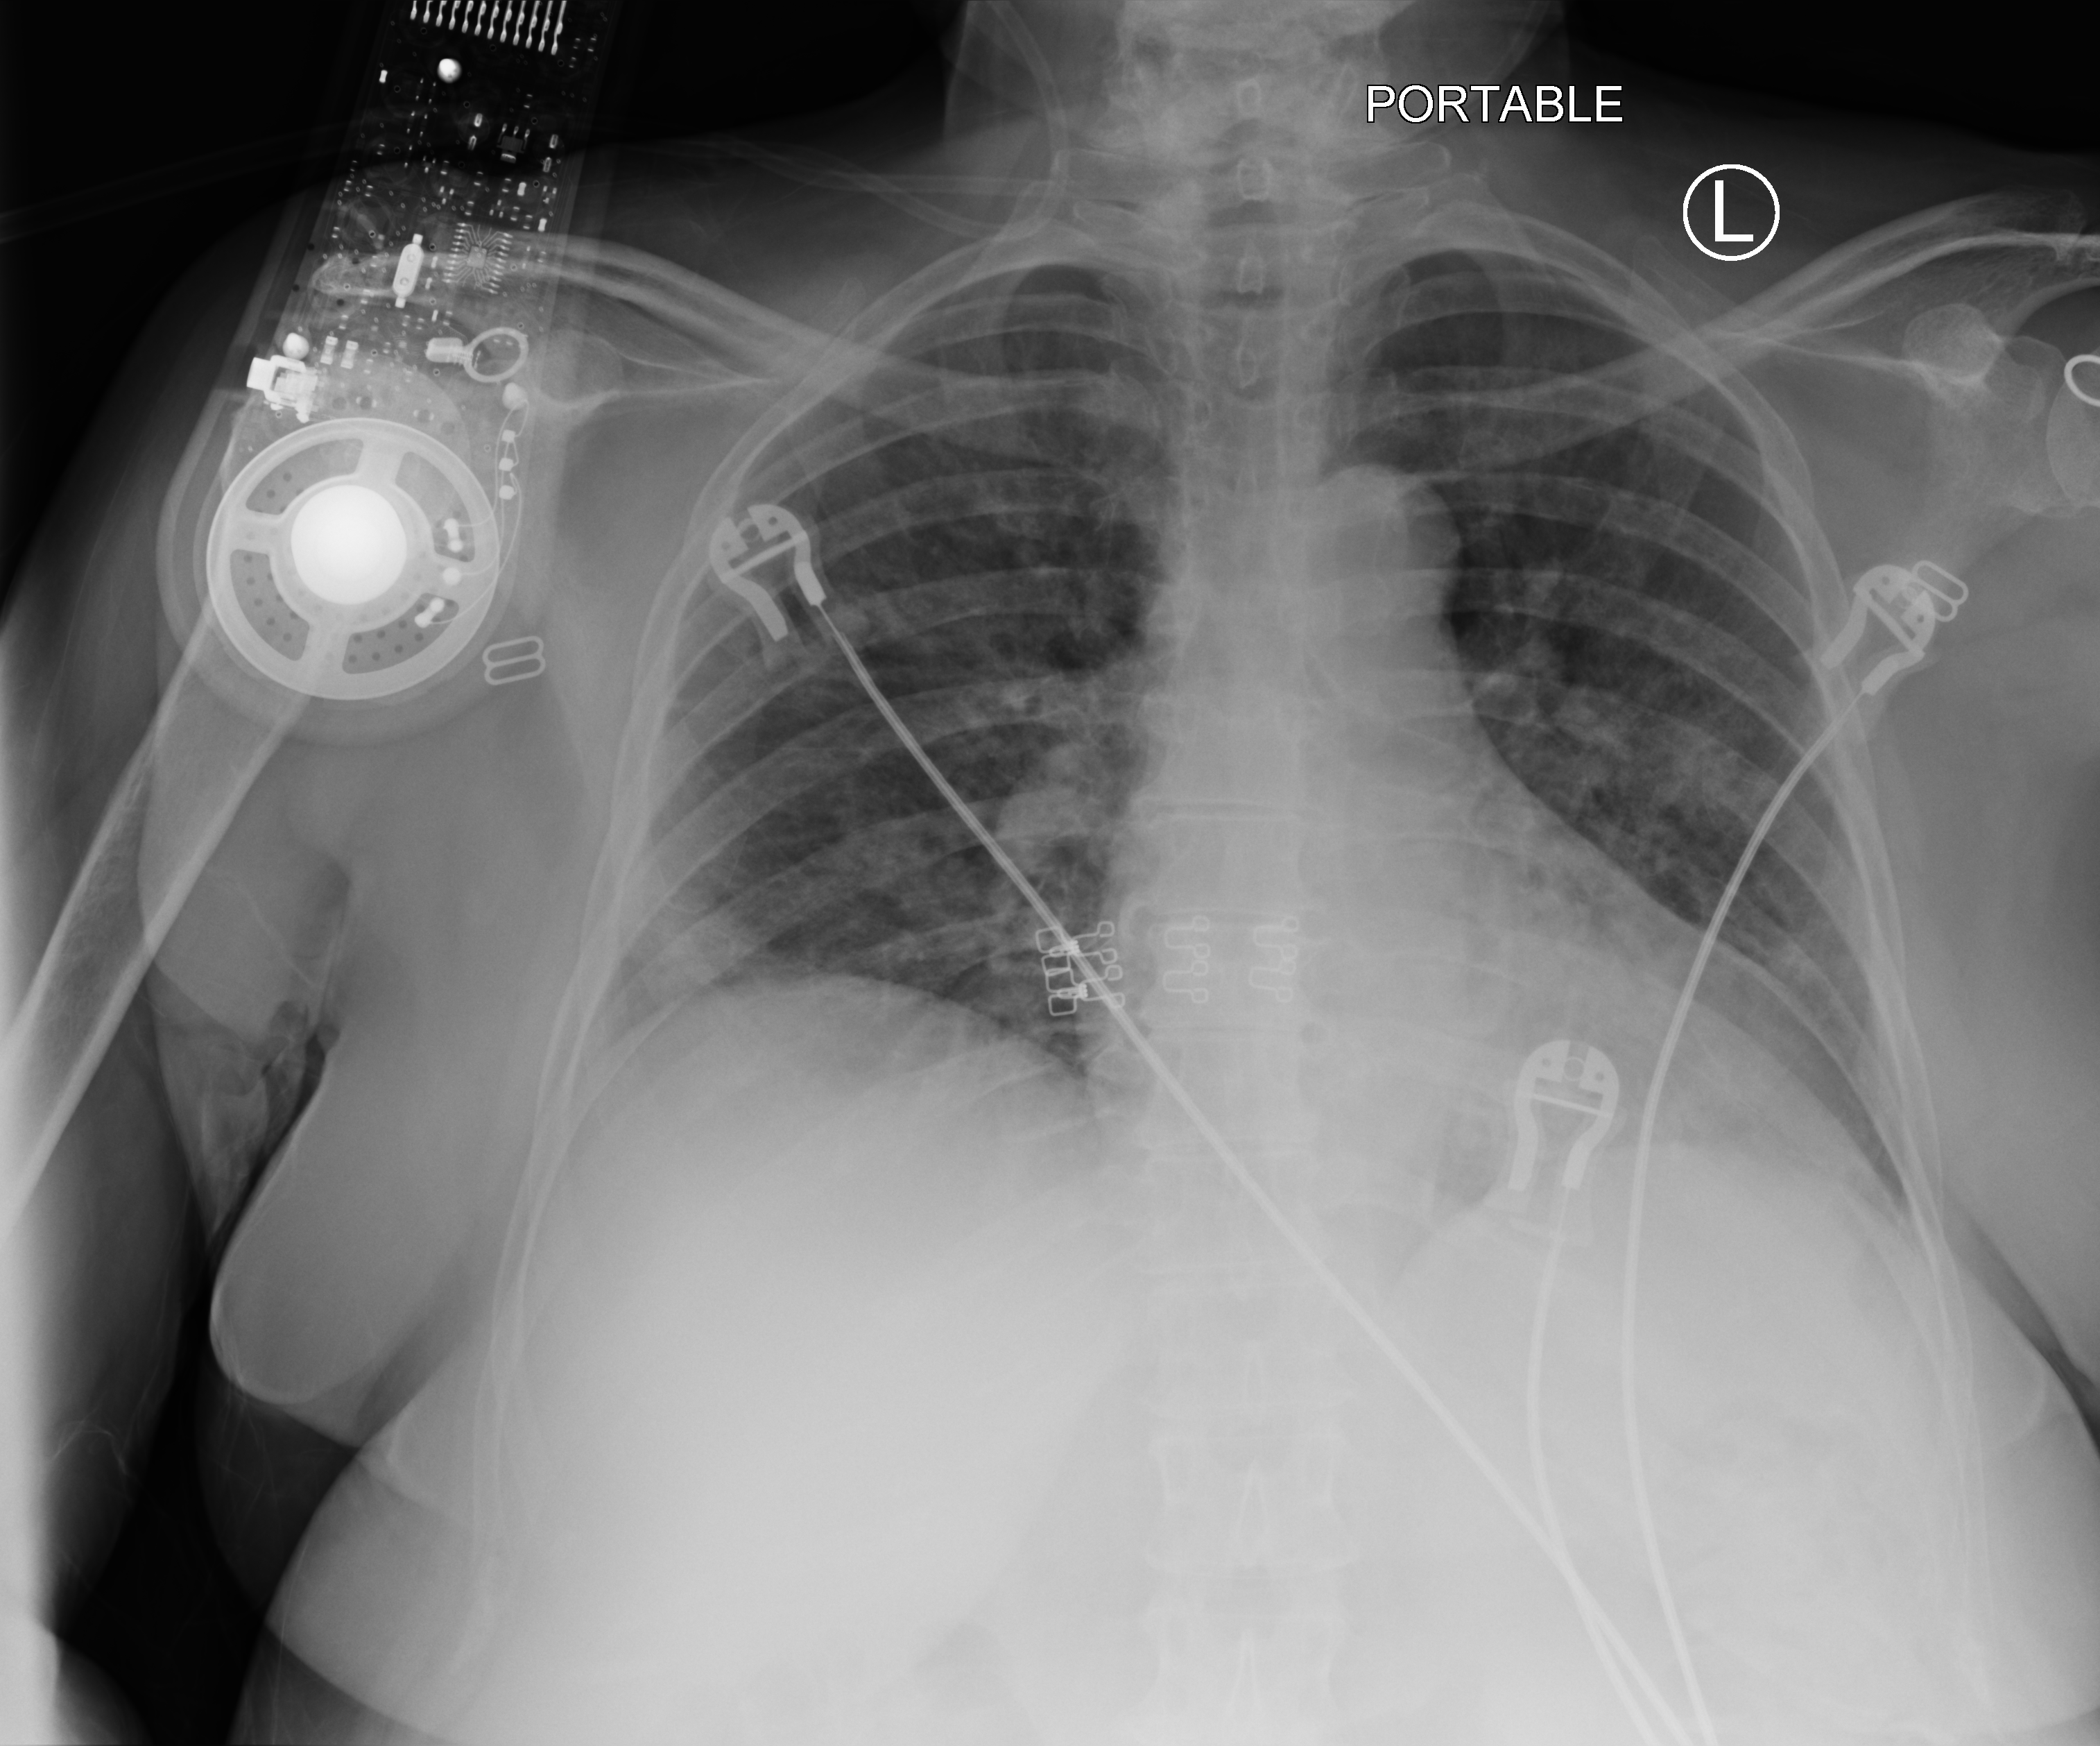
Portable chest radiograph. Patient hospitalised with COVID-19; female, aged 60–74 years.
Admission-level facts for this patient (not findings on this image; timing relative to this image not recorded): mechanically ventilated during this hospital stay: no.